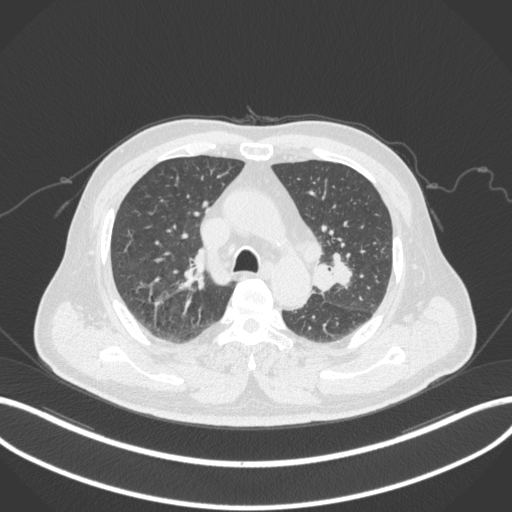
Chest CT, one axial slice; slice 204 of 286 in the series (ordered by position); reconstruction kernel B31f; 120 kVp; lung window (W 1500 / L -600 HU); 1 mm slice thickness; 512 × 512 image matrix. Patient: male, 67 years. From the clinical record (not read from this slice): clinical TNM (as recorded): T2a N1 M0.
Structures marked on this image (bounding box drawn by a radiologist):
- lung tumour (recorded histology: adenocarcinoma): bounding box (x1, y1, x2, y2) in pixels: (314, 259, 353, 294)